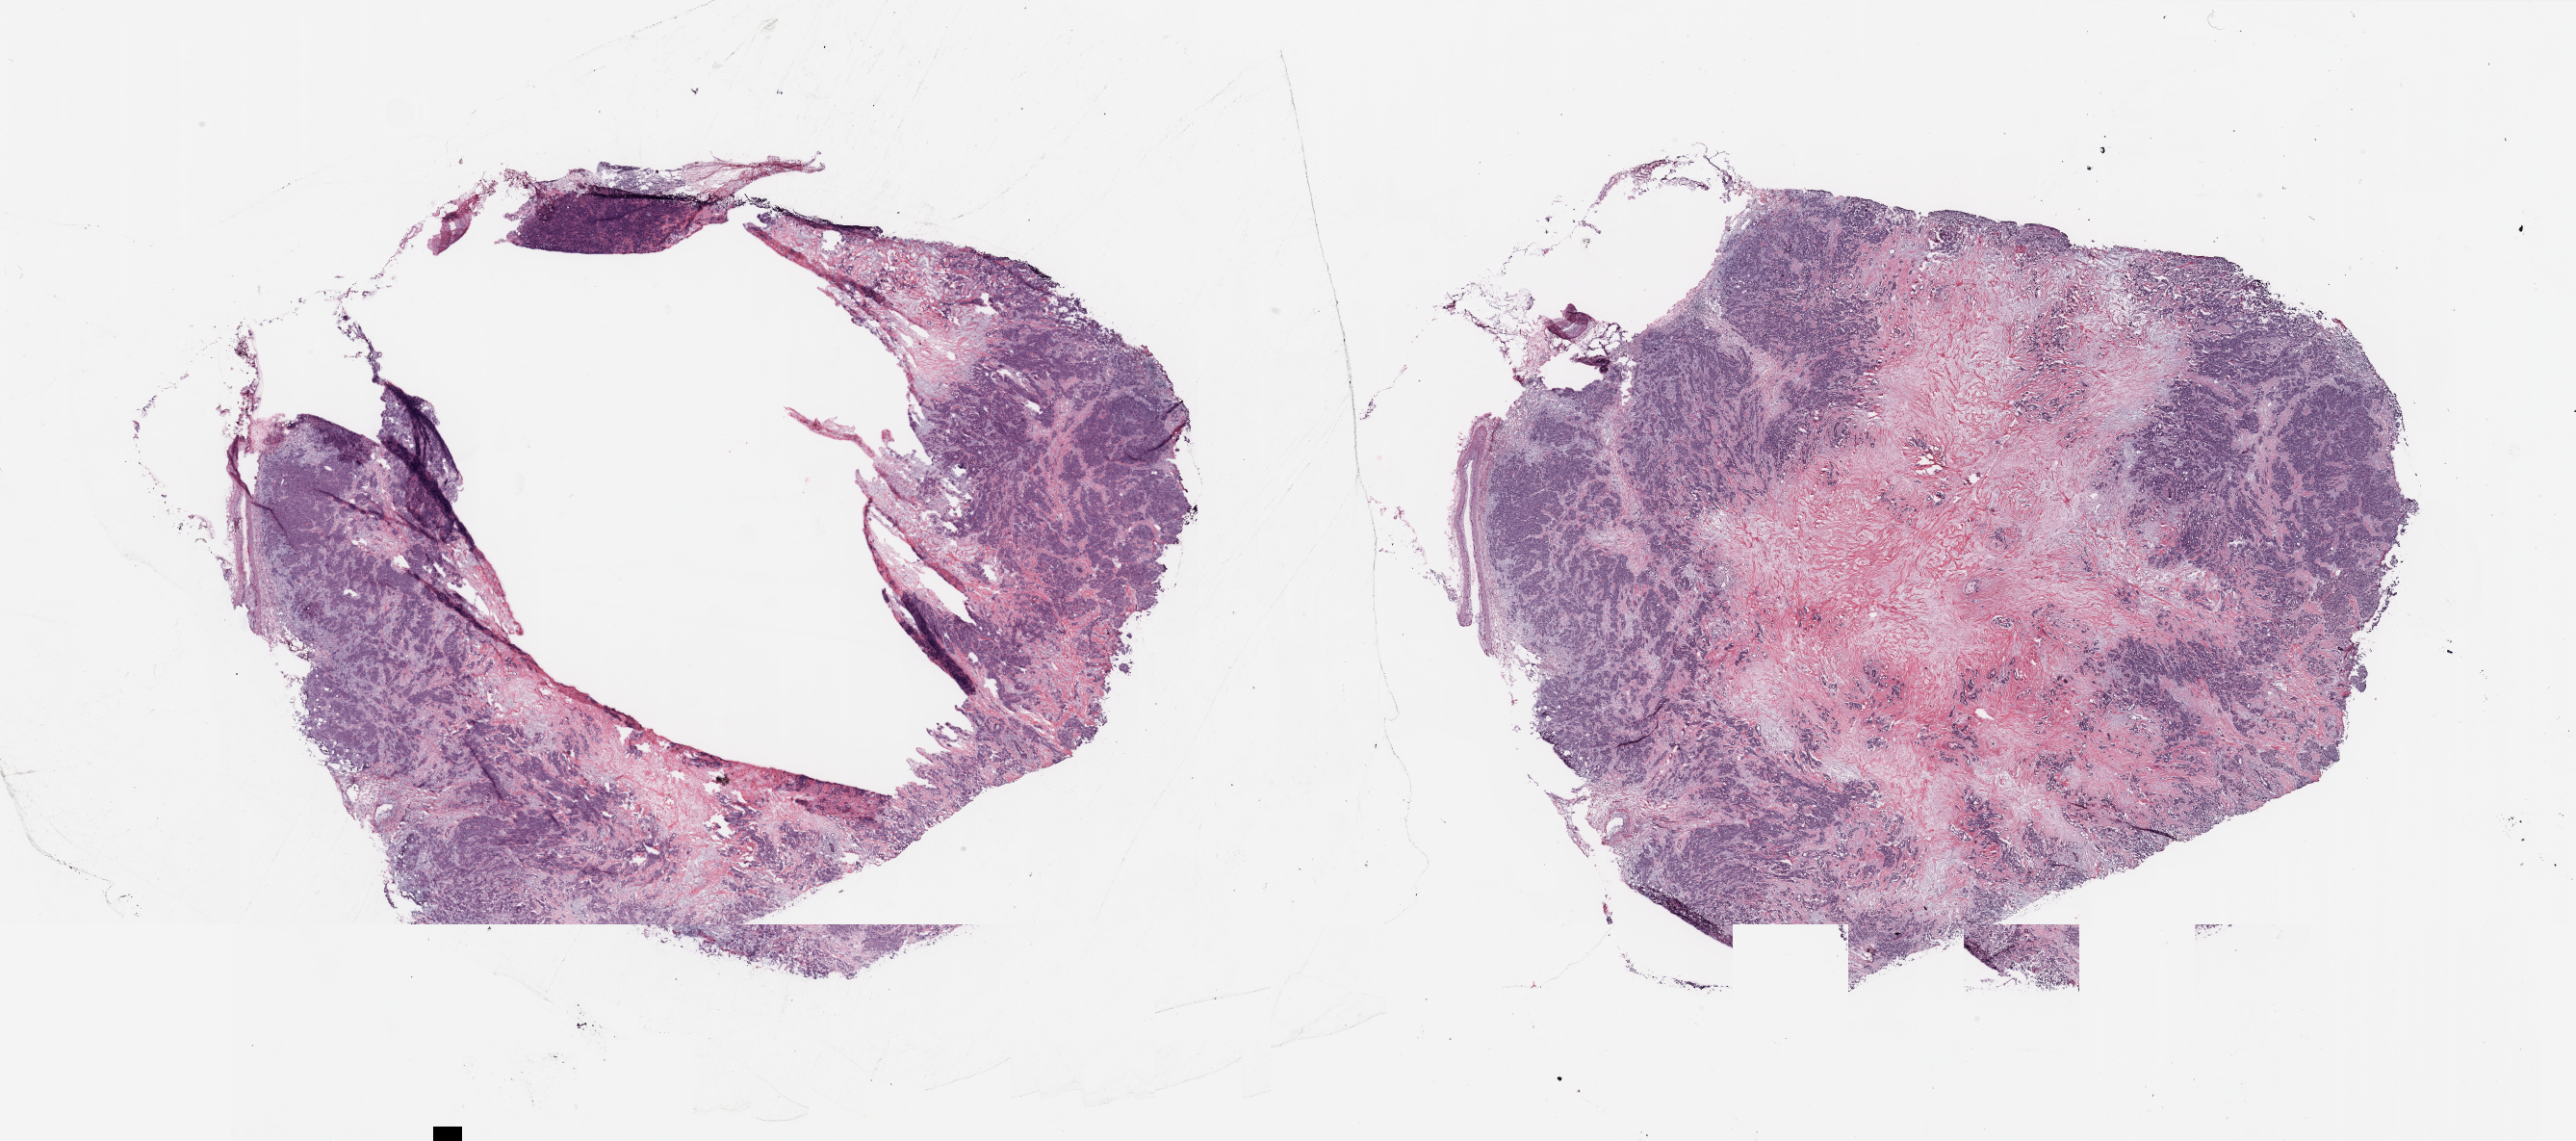
Digitized H&E-stained tissue section (whole slide), a low-resolution overview of the entire scanned area, about 42.3 x 18.7 mm (acquisition: 20x scan); breast, tissue type not recorded.
Patient diagnosis (cohort enrolment): breast cancer (breast).